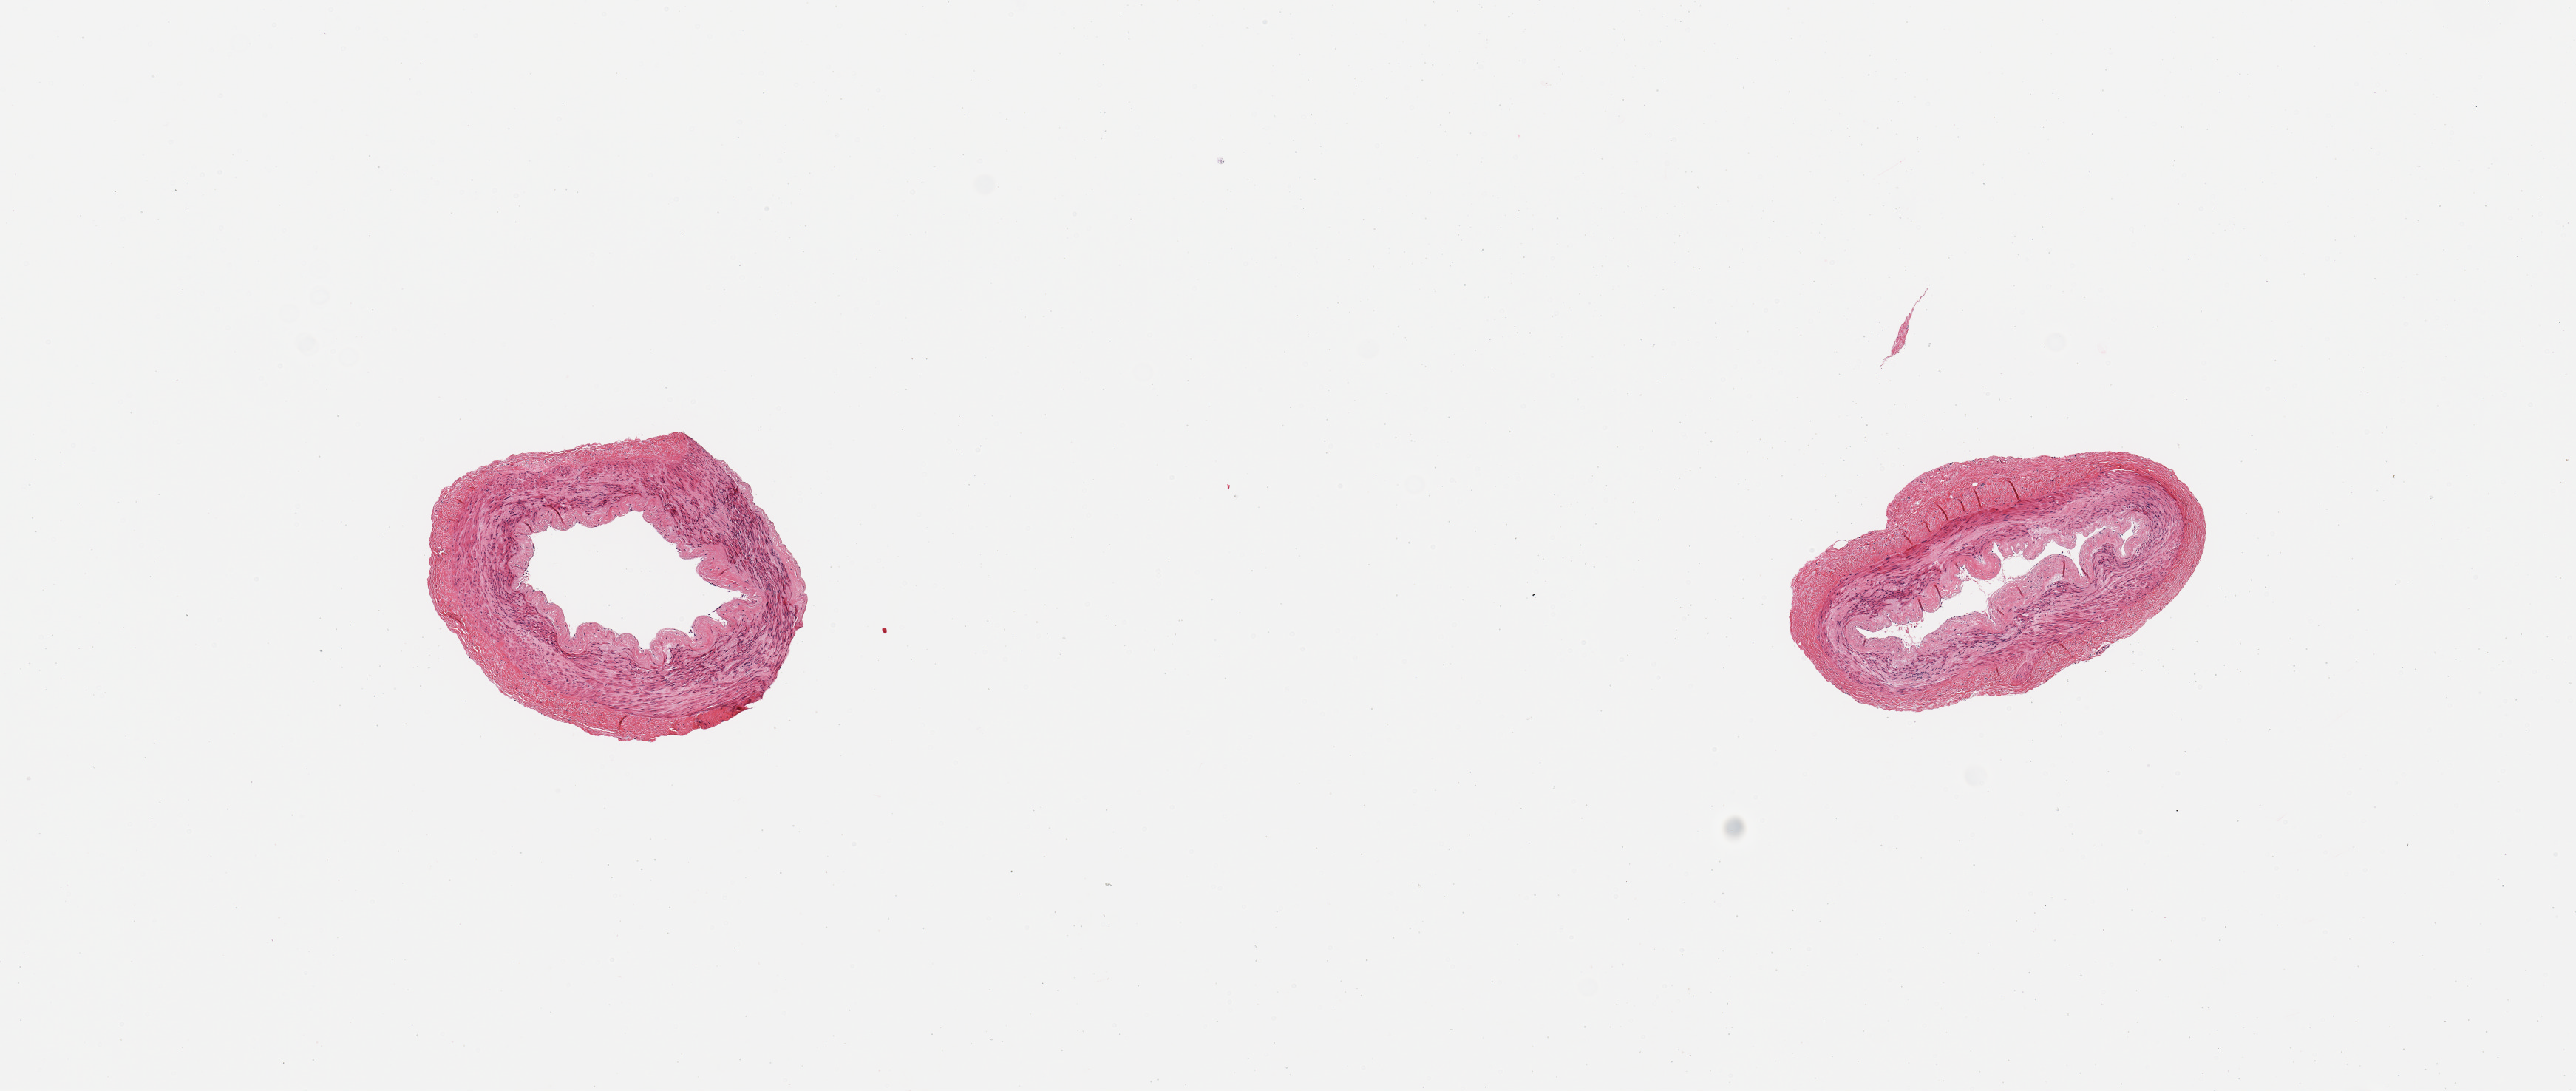
Whole-slide image, H&E stain, whole scanned area (about 13.8 x 5.8 mm, slide scanned at 20x) shown as a low-resolution overview. PAXgene-fixed, paraffin-embedded tissue. Section of tibial artery (target tissue). Donor tissue sample. Donor: female.
Pathologist's review note for this sample: 2 pieces; well trimmed, no lesions.